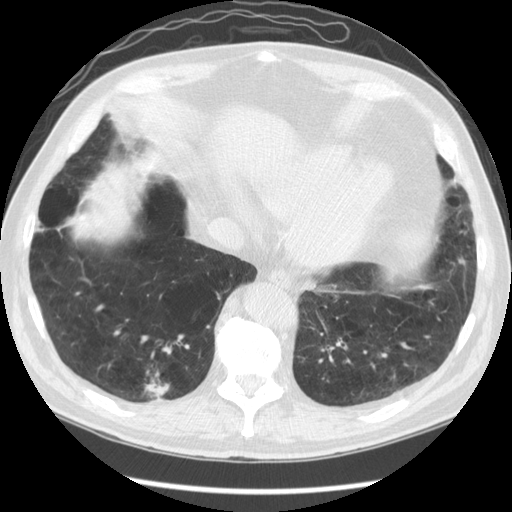
Low-dose screening chest CT, one axial slice; slice 41 of 141 in the series (ordered by position); reconstruction kernel STANDARD; 120 kVp; lung window (W 1500 / L -600 HU); 2.5 mm slice thickness; 512 × 512 image matrix, field of view 370 × 370 mm.
Outlined on this slice (manually delineated by an expert):
- lesion 1 (tumor, lower lobe of right lung): bounding box (x1, y1, x2, y2) in pixels: (145, 385, 170, 396)